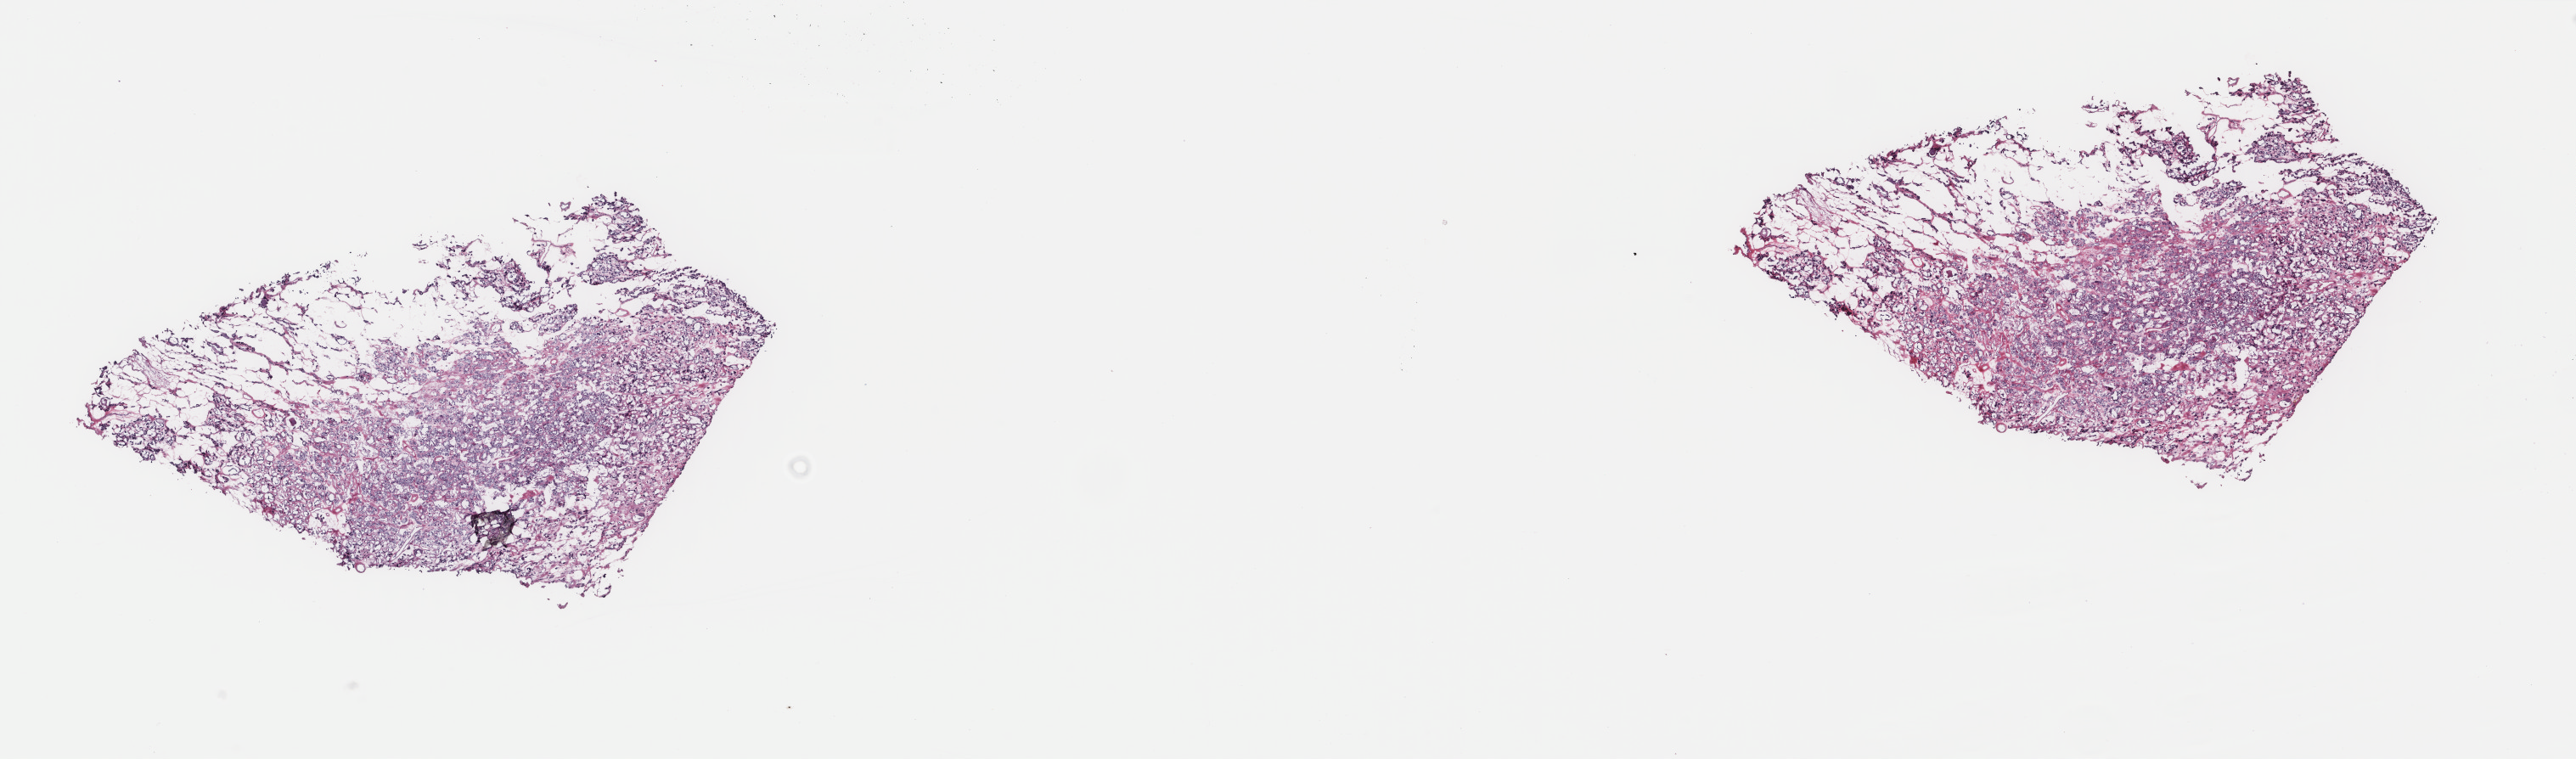
H&E whole-slide image — shown as a low-resolution overview of the whole scanned area (about 24.1 x 7.1 mm), frozen section, primary tumour sample from the thyroid. Female, age 68 years at initial diagnosis. Composition of this section per pathologist review: tumour cells 100%, tumour nuclei 90%, normal cells 0%, stromal cells 0%, necrosis 0%. Inflammatory infiltration, as recorded: lymphocyte infiltration 0%, monocyte infiltration 0%, neutrophil infiltration 0%.
• AJCC pathologic stage: II (5th edition)
• laterality: right
• diagnosis: Papillary carcinoma, follicular variant (thyroid gland)